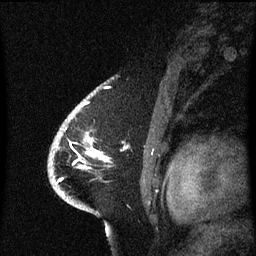
Breast MRI (dynamic contrast-enhanced), one sagittal slice. Position 47 of 60 along the scan axis. Dynamic contrast-enhanced series, image 2 of 3 at this slice position (ordered by acquisition). 1.5 T. TE 4.2 ms, TR 8.4 ms. 2.1 mm slice thickness. 256 × 256 image matrix, field of view 200 × 200 mm. Patient: female, 53 years. From the clinical record (not read from this slice): setting: breast cancer imaged before/during neoadjuvant chemotherapy; receptor status: HR-positive, HER2-negative.
Structures marked on this image (semi-automatically segmented with operator editing):
- analysis volume of interest (the breast-tissue region the enhancement analysis was run in; not a lesion): bounding box <49,108,109,201> (left, top, right, bottom; pixels)
- tumour enhancement mask (voxels above the 70 % enhancement threshold inside the analysis volume of interest): <59,150,104,183>